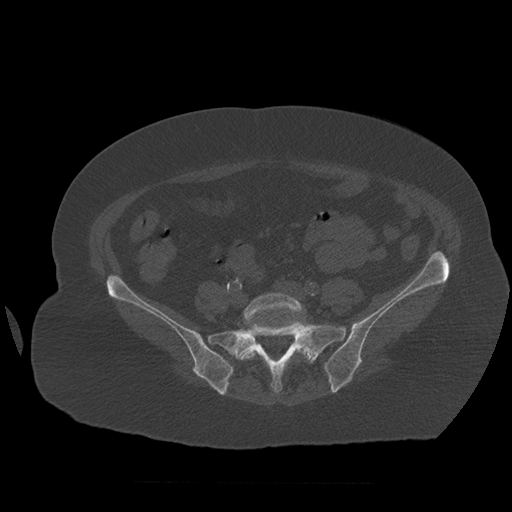
CT including the spine, one axial slice; slice 171 of 399 in the series (ordered by position); reconstruction kernel STANDARD; 120 kVp; bone window (W 1800 / L 400 HU); 512 × 512 image matrix. Patient age 81 years. Case-level facts recorded for this patient, not image findings: primary cancer: renal; vertebrae with lytic lesions (as recorded): L1.
Outlined on this slice (semi-automatic segmentation, software-assisted and operator-edited):
- L5 vertebra: bounding box [x1, y1, x2, y2] px = [240, 293, 313, 361]